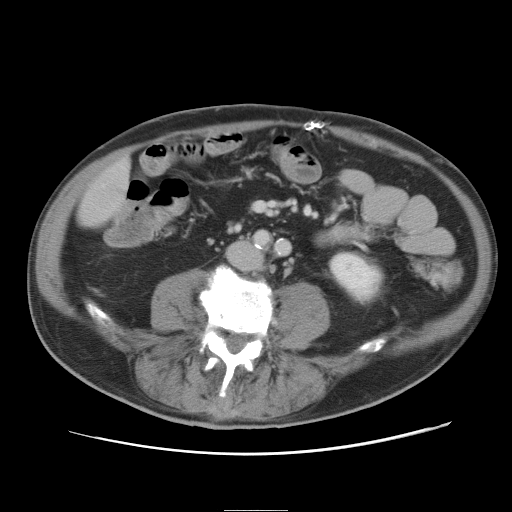
Contrast-enhanced abdominal CT, one axial slice. Position 1 of 89 along the scan axis. 120 kVp. Intravenous contrast given. Soft-tissue window (W 400 / L 40 HU). 5 mm slice thickness. 512 × 512 image matrix. Male patient, age 69 years. Case-level facts recorded for this patient, not image findings: diagnosis: colorectal cancer liver metastases, imaged before liver resection; multiple liver metastases: no; largest metastasis: 8.5 cm; disease in both lobes: no.
Structures marked on this image (outlined manually by an expert reader):
- liver: bounding box [x1, y1, x2, y2] px = [78, 163, 131, 227]
- planned liver remnant (the part of the liver to remain after resection): [79, 163, 130, 227]